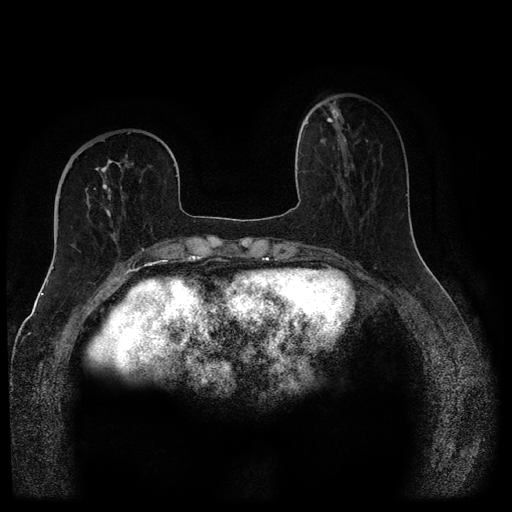
Breast MRI (dynamic contrast-enhanced, multi-phase), one axial slice; position 36 of 116 along the scan axis; dynamic contrast-enhanced series, time point 2 of 5 at this slice position (early post-contrast); 1.5 T; TE 2.6 ms, TR 5.4 ms; 2 mm slice thickness; 512 × 512 image matrix. Patient: female, 68 years.
Outlined on this slice (semi-automatically segmented with operator editing):
- breast lesion (labelled benign in the annotation): box from (x=321, y=102) to (x=350, y=142) px